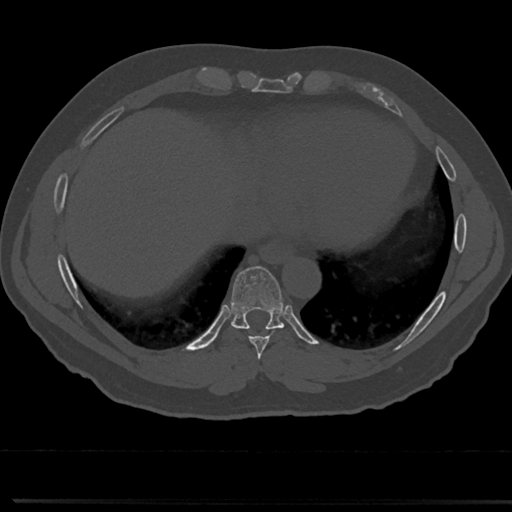
CT including the spine, one axial slice; slice 326 of 817 in the series (ordered by position); bone window (W 1800 / L 400 HU); 0.5 mm slice thickness; 512 × 512 image matrix, field of view 355 × 355 mm. Patient: male, 61 years. From the clinical record (not read from this slice): primary cancer: prostate.
Structures marked on this image (semi-automatic segmentation, software-assisted and operator-edited):
- T7 vertebra: bounding box [x1, y1, x2, y2] px = [258, 354, 266, 376]
- T8 vertebra: [212, 270, 310, 357]